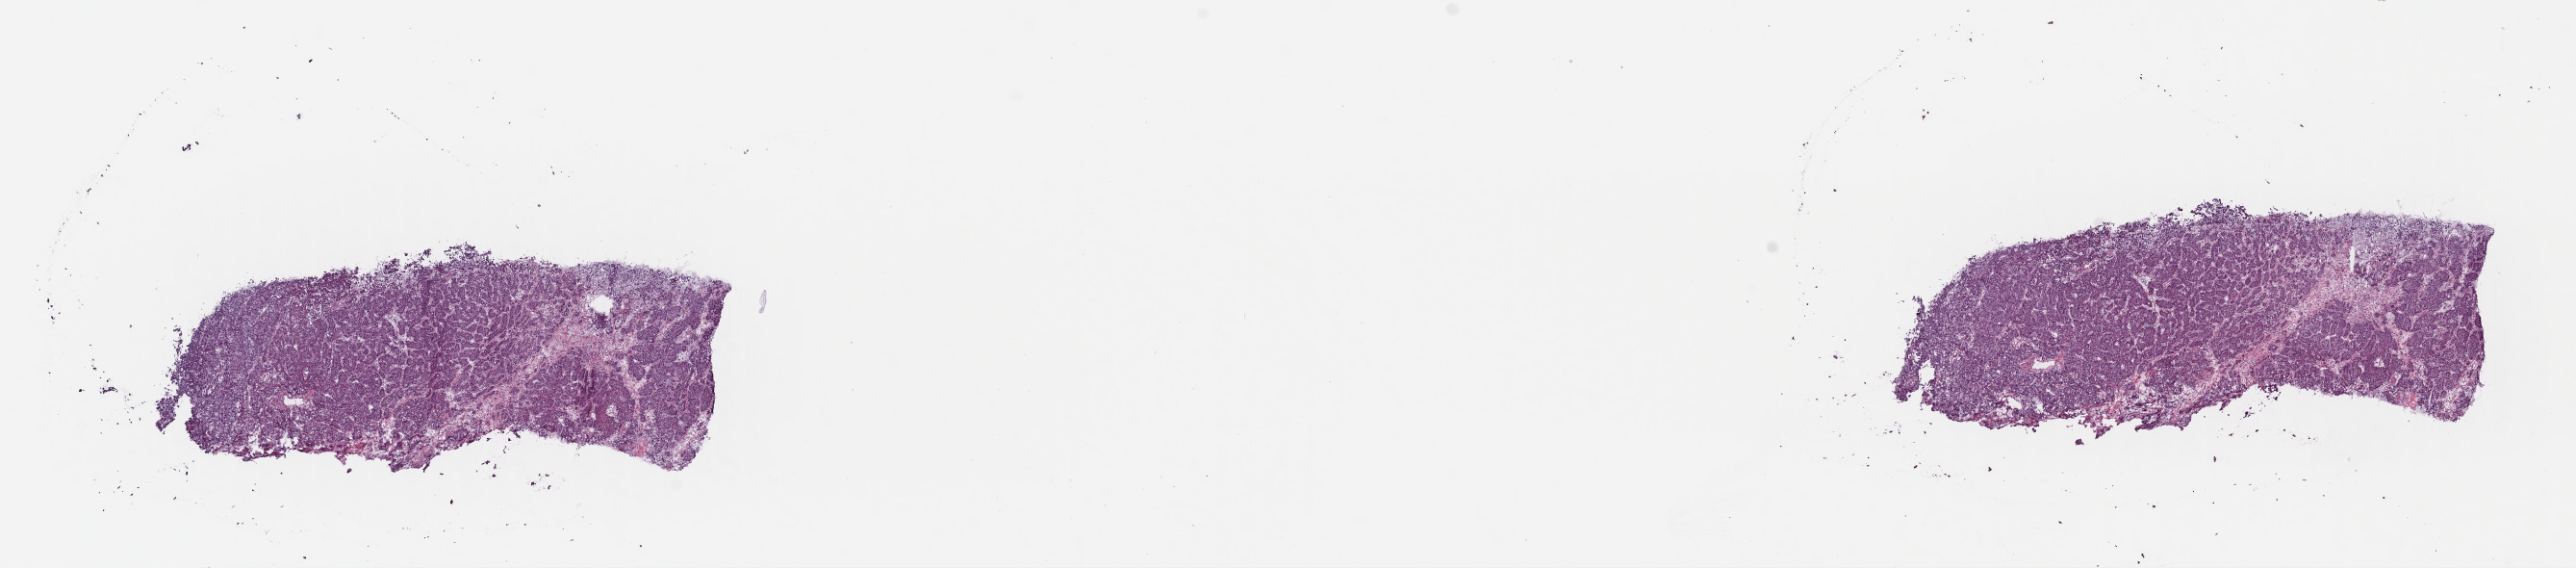
Whole-slide histology image, H&E-stained — shown as a low-resolution overview of the whole scanned area (about 21.0 x 4.6 mm, acquisition: 40x scan), frozen section, sample: primary tumour, liver. Patient: male, age at initial diagnosis 50 years. Histologic grade: G2 (moderately differentiated). Slide review estimates, as recorded: tumour cells 100%, tumour nuclei 80%, normal cells 0%, stromal cells 0%, necrosis 0%. Infiltration values recorded for this section: lymphocyte infiltration 2%, monocyte infiltration 0%, neutrophil infiltration 0%.
- histologic diagnosis: Hepatocellular carcinoma, NOS
- AJCC pathologic stage: IIIA (7th edition)